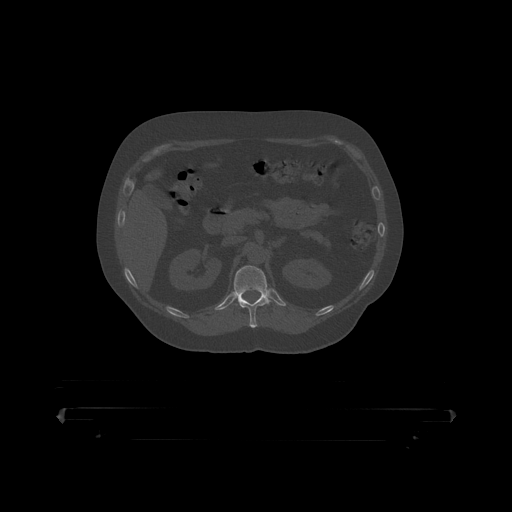
CT including the spine, one axial slice; position 169 of 390 along the scan axis; 120 kVp; bone window (W 1800 / L 400 HU); 512 × 512 image matrix, field of view 650 × 650 mm. Patient: male, 60 years. From the clinical record (not read from this slice): primary cancer: prostate.
Outlined on this slice (semi-automatic segmentation, software-assisted and operator-edited):
- T12 vertebra: box from (x=232, y=266) to (x=273, y=319) px